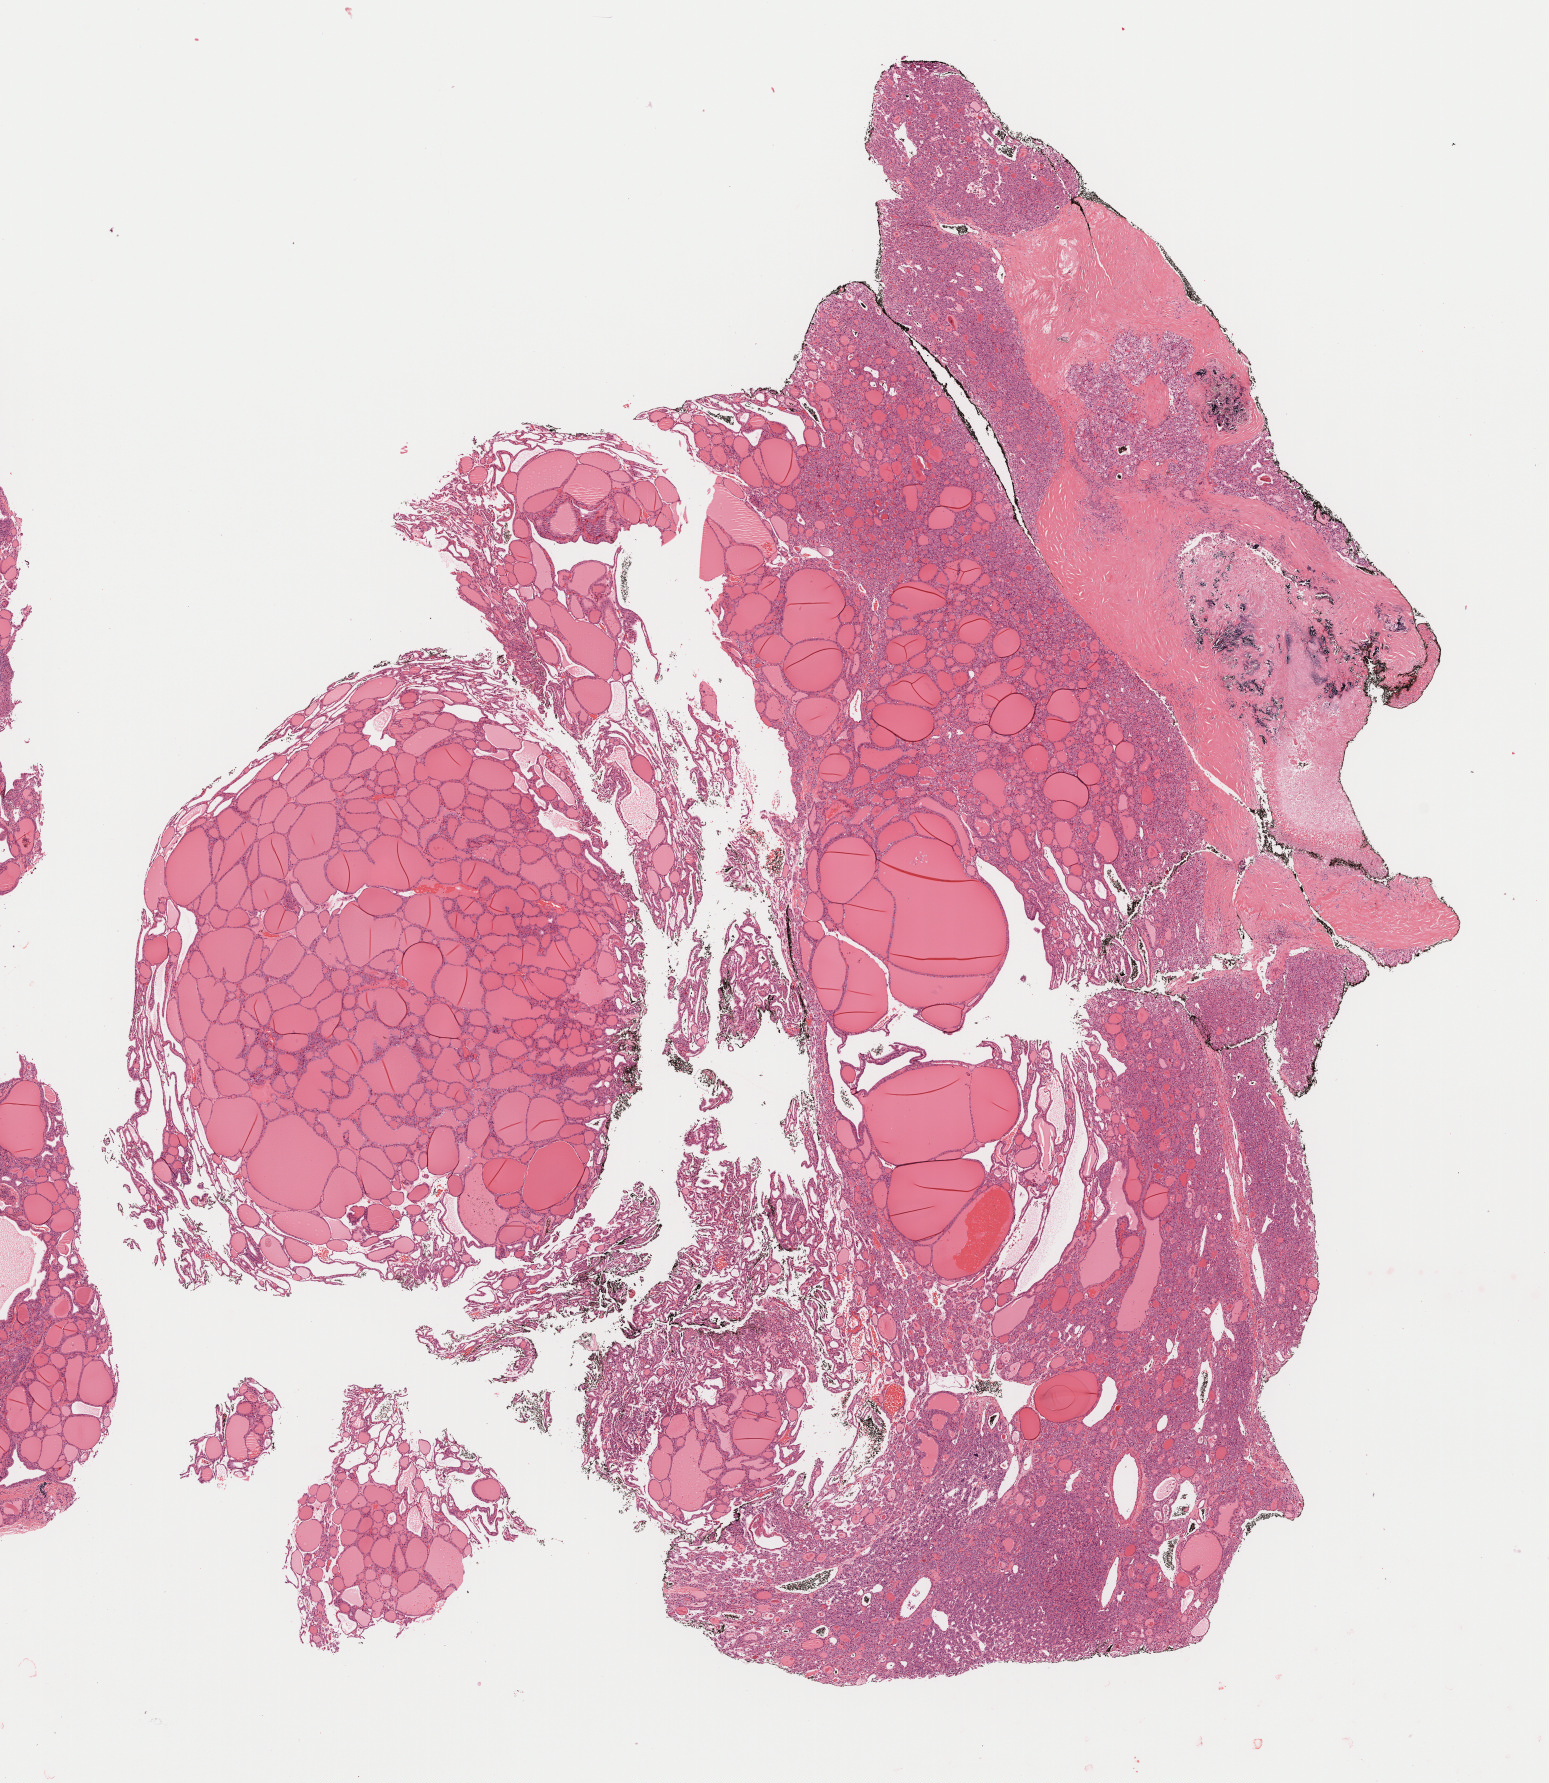
H&E-stained whole-slide image — low-resolution overview of the scanned area, about 12.5 x 14.4 mm. Formalin-fixed paraffin-embedded (FFPE) diagnostic section. Thyroid, primary tumour sample. Patient: male, age at initial diagnosis 35 years.
AJCC pathologic stage: I (6th edition). Diagnosis: Papillary carcinoma, follicular variant. TNM: T3 NX MX. Laterality: left.